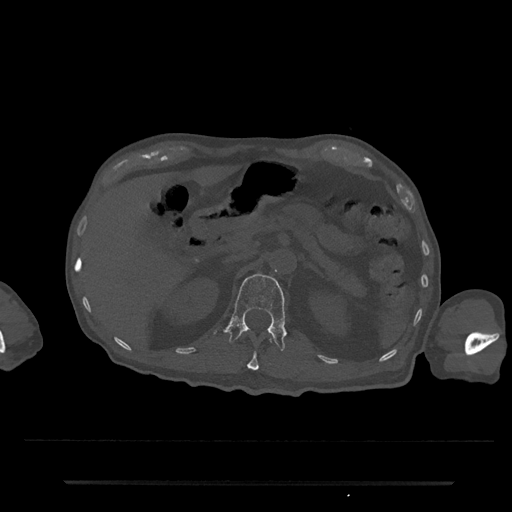
CT including the spine, one axial slice. Slice 149 of 797 in the series (ordered by position). Reconstruction kernel Br40s/3. Bone window (W 1800 / L 400 HU). 512 × 512 image matrix, field of view 427 × 427 mm. Patient: male, 74 years. Case-level facts recorded for this patient, not image findings: primary cancer: prostate.
Outlined on this slice (semi-automatic segmentation, software-assisted and operator-edited):
- L1 vertebra: bounding box [x1, y1, x2, y2] px = [225, 274, 286, 353]
- T12 vertebra: [247, 339, 272, 371]